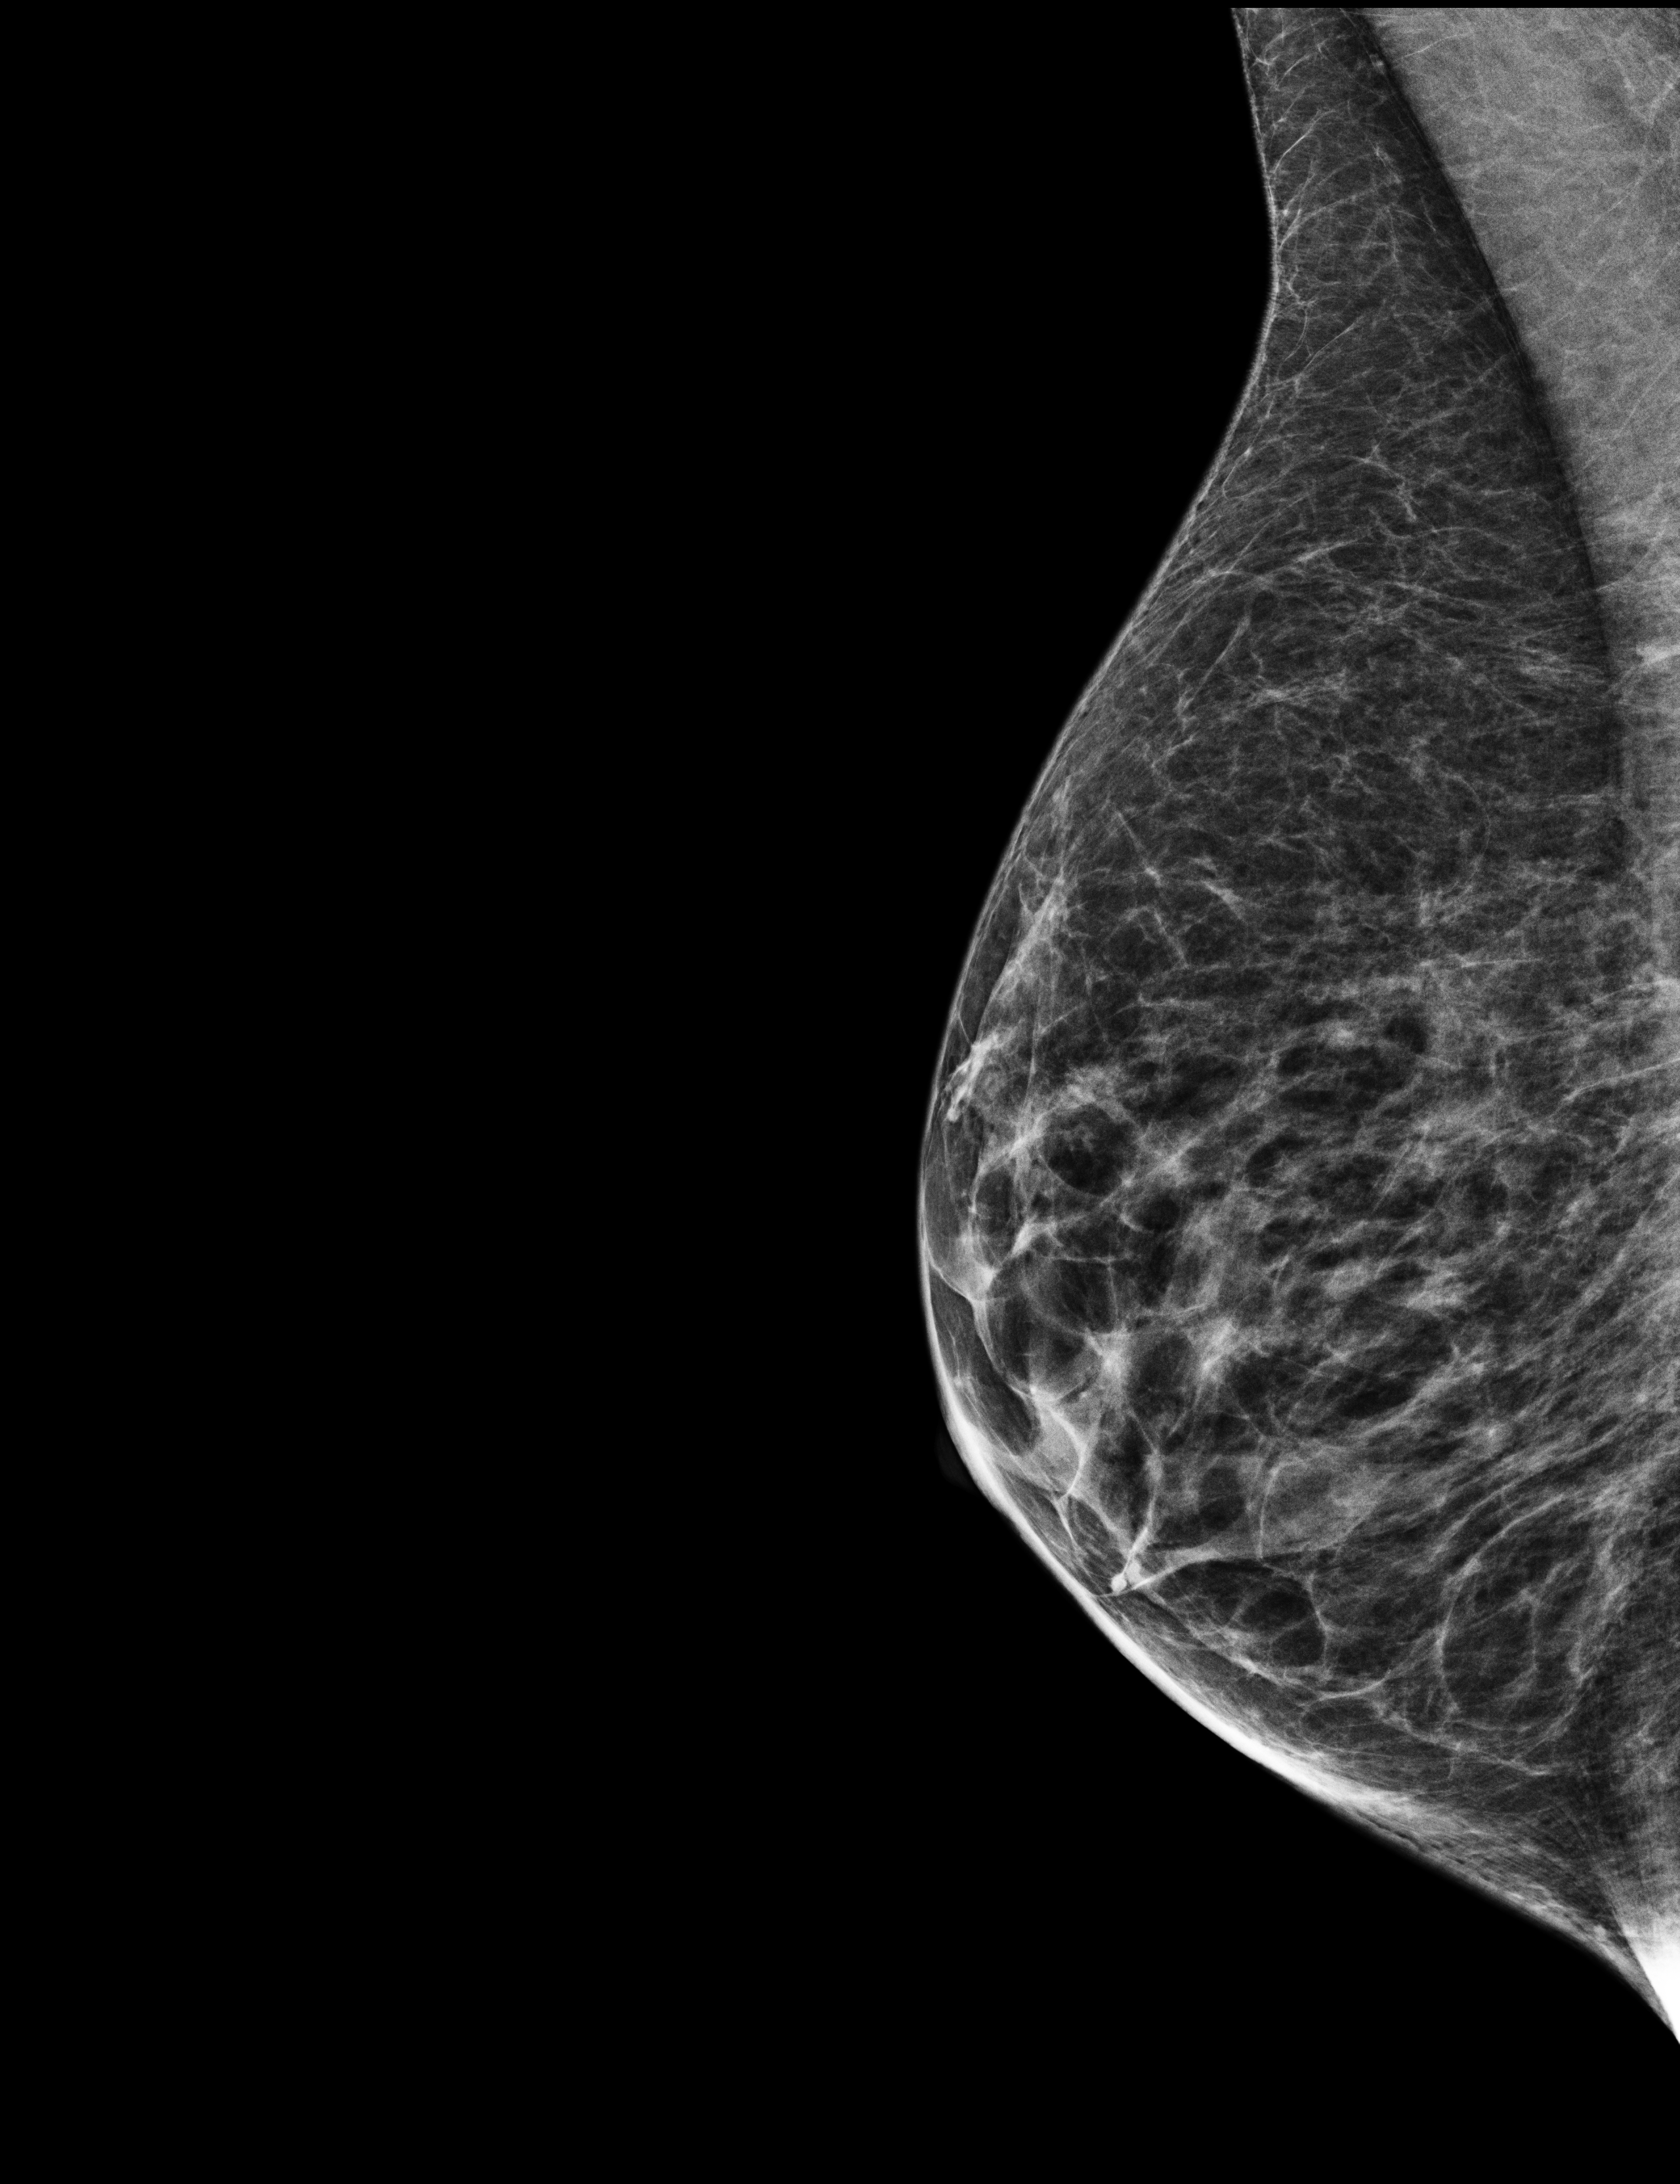
Screening examination.
Image type: full-field digital mammogram. Breast: right. Projection: mediolateral oblique (MLO) view.